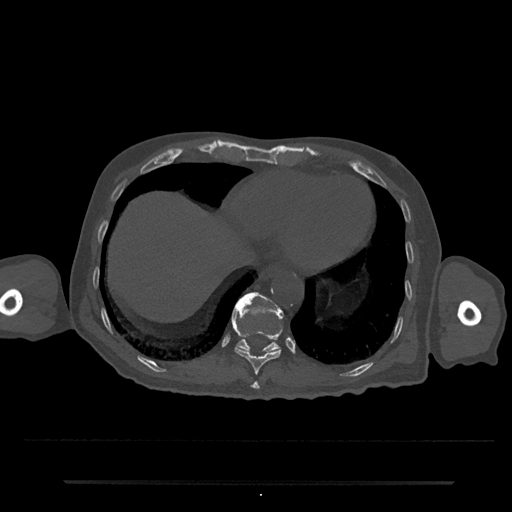
CT including the spine, one axial slice. Reconstruction kernel Br40s/3. 120 kVp. Bone window (W 1800 / L 400 HU). 0.5 mm slice thickness. 512 × 512 image matrix. Male patient, age 74 years. Case-level facts recorded for this patient, not image findings: primary cancer: prostate.
Outlined on this slice (semi-automatically segmented with operator editing):
- T10 vertebra: bounding box [x1, y1, x2, y2] px = [231, 315, 283, 375]
- T11 vertebra: [233, 292, 284, 353]
- T9 vertebra: [251, 382, 260, 390]